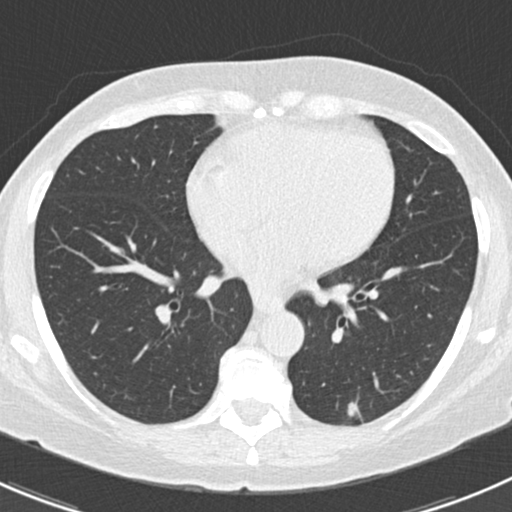
Chest CT (low-dose screening protocol), one axial image, second annual screen, lung window (W 1500 / L -600 HU), 2 mm slice thickness, standard (soft-tissue) reconstruction kernel (B30f), slice 88 of 166 in the series, 512 × 512 image matrix. Female participant, aged 64 years at enrolment.
Lesion marked by an expert reader, bounding box [x1, y1, x2, y2] px = [330, 394, 377, 431]. Screening reader's record for this exam (one nodule recorded; not confirmed to be the boxed lesion): non-calcified nodule or mass ≥4 mm, left lower lobe, 8 × 3 mm, poorly defined margins, soft tissue attenuation, pre-existing on the prior screen: yes; interval growth: no. Official screen result: positive, no significant change: stable abnormalities potentially related to lung cancer, unchanged since the prior screening exam. Later outcome: lung cancer diagnosed 101 days after this screen — adenocarcinoma, NOS, left lower lobe, poorly differentiated (G3), stage IA (AJCC 6th edition), 8 mm at pathology.